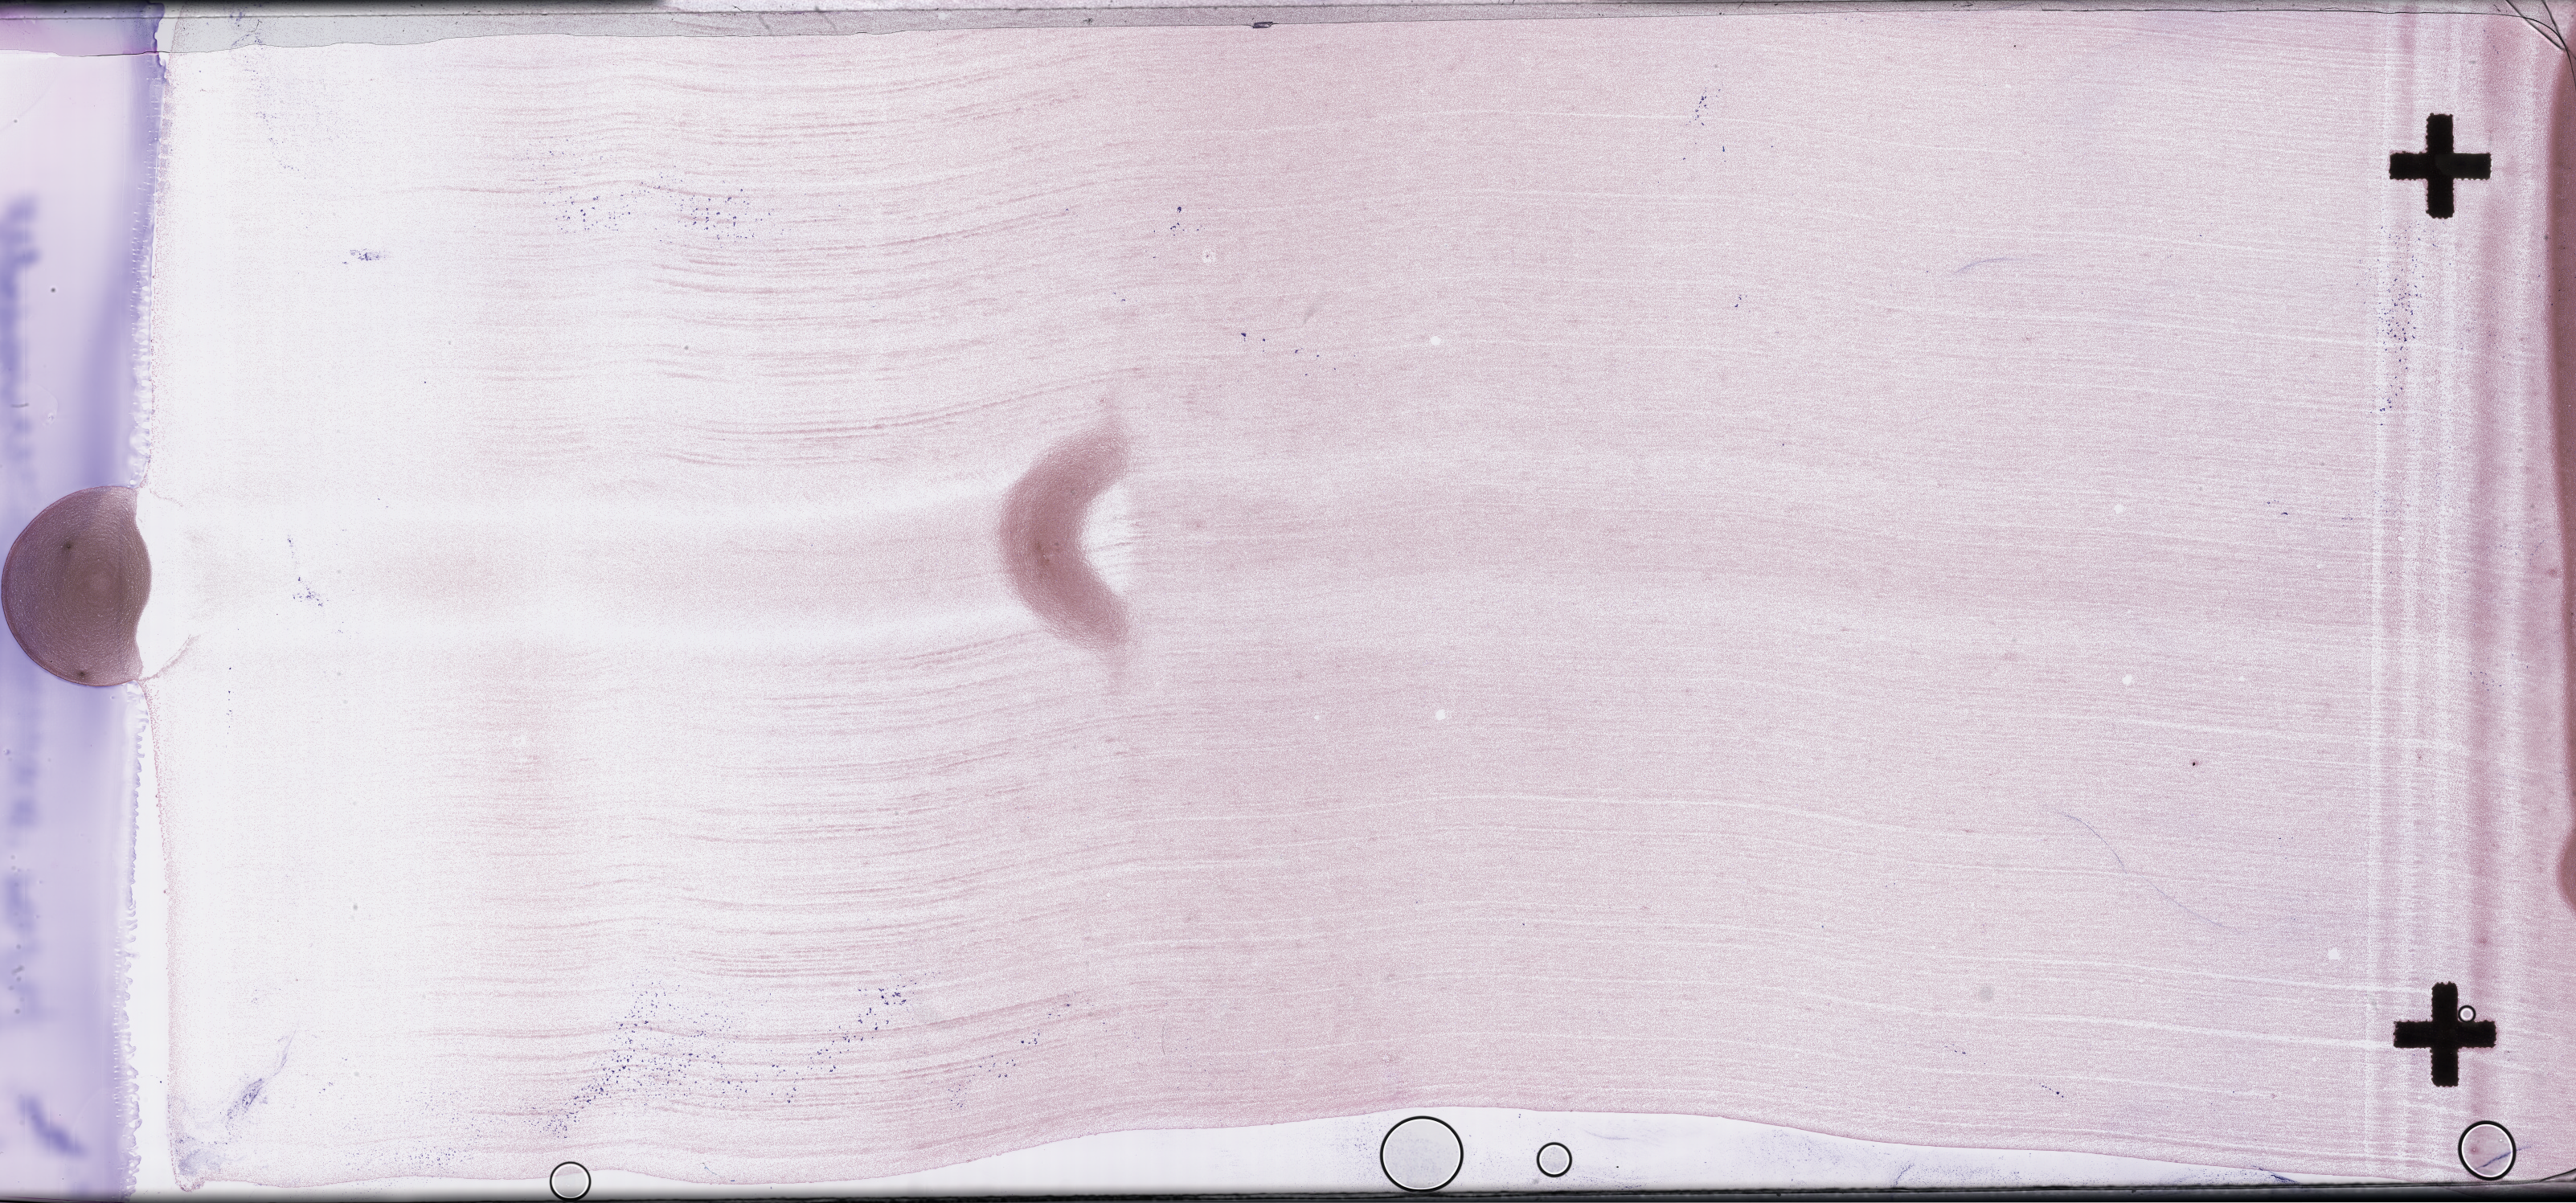
Wright–Giemsa-stained bone marrow smear, whole-slide image — shown as a low-resolution overview of the whole scanned area (about 51.8 x 24.2 mm); EDTA-anticoagulated smear. Patient sex: male.
Patient diagnosis: Plasma Cell Myeloma.